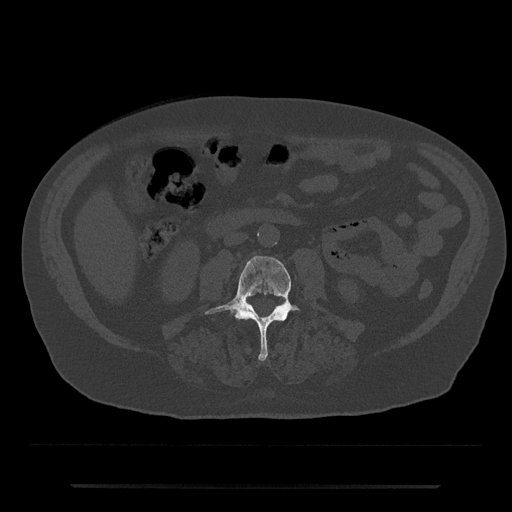
CT including the spine, one axial slice. 120 kVp. Bone window (W 1800 / L 400 HU). 512 × 512 image matrix, field of view 434 × 434 mm. Male patient, age 80 years. Case-level facts recorded for this patient, not image findings: primary cancer: prostate.
Annotated regions visible in this slice (semi-automatic segmentation, software-assisted and operator-edited):
- L3 vertebra: bounding box [x1, y1, x2, y2] px = [205, 256, 299, 361]